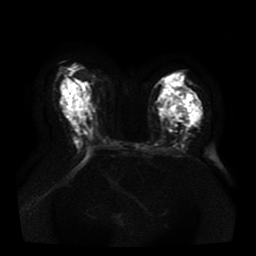
Breast MRI, one axial slice. Position 24 of 41 along the scan axis. Diffusion-weighted series; image 2 of 4 stored at this slice position (different b-values; order by instance number). 1.5 T. 5 mm slice thickness. 256 × 256 image matrix. Female patient.
Structures marked on this image (outlined manually by an expert reader):
- tumour on diffusion-weighted imaging: bounding box (x1, y1, x2, y2) in pixels: (168, 94, 201, 117)